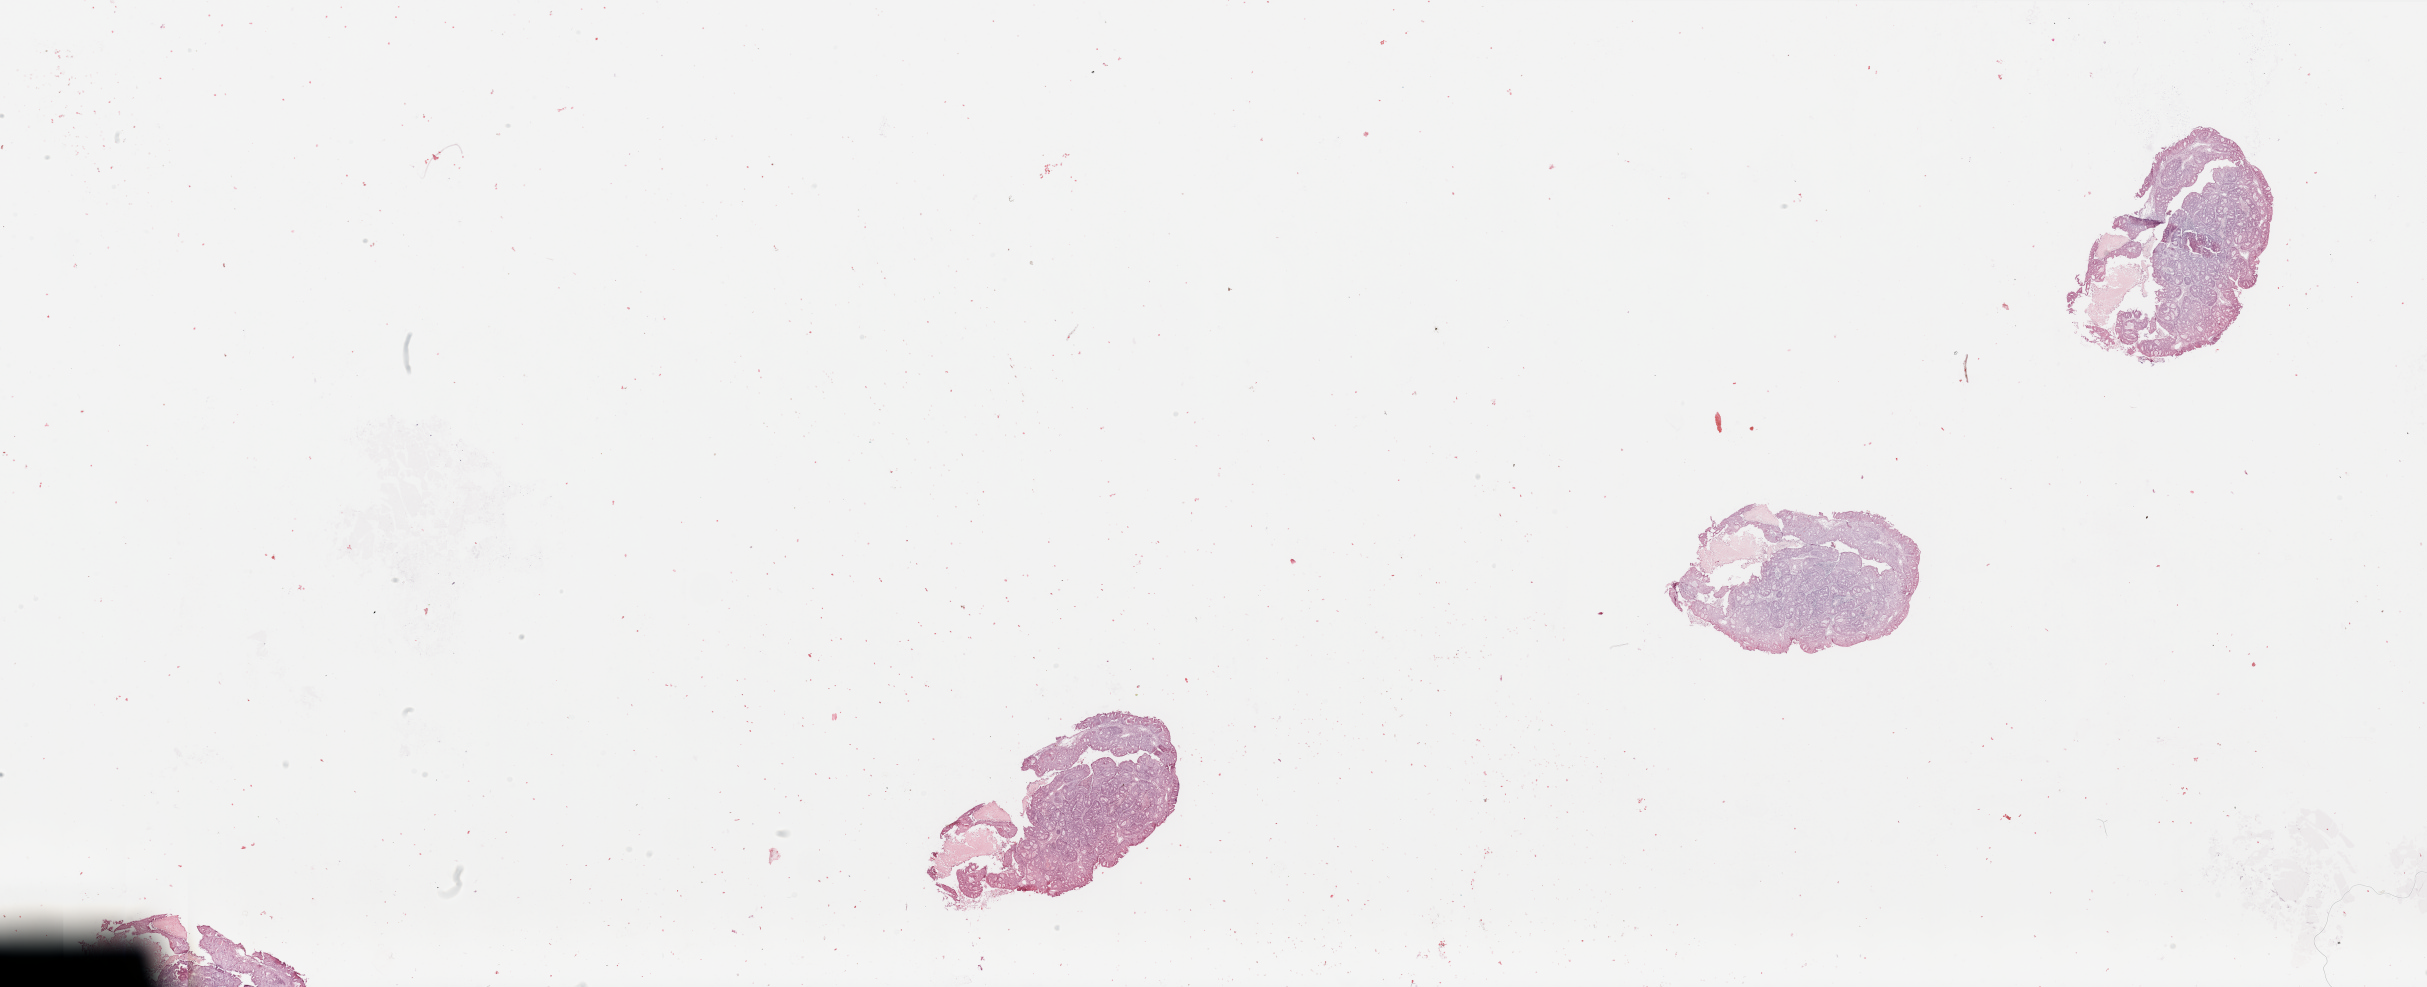
H&E whole-slide image — whole scanned area (about 38.4 x 15.6 mm) shown as a low-resolution overview. Tumour tissue sample, sampled site: uterus. Patient: female, age 60 years. Histologic grade: G2 (moderately differentiated). Slide review estimates, as recorded: tumour nuclei 90%, necrosis 5%.
Primary tumour site (as recorded): anterior endometrium. Diagnosis: Endometrioid adenocarcinoma, NOS. AJCC pathologic stage: IIIB.